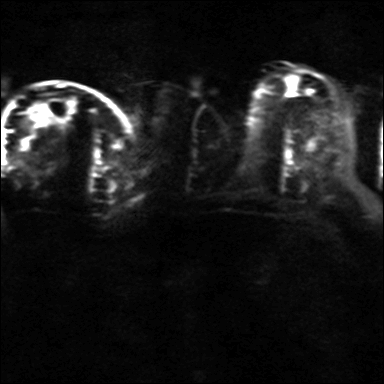
Breast MRI, one axial slice; slice 16 of 36 in the series (ordered by position); diffusion-weighted series; image 2 of 4 stored at this slice position (different b-values; order by instance number); 3 T; 4 mm slice thickness; 384 × 384 image matrix. Female patient.
Structures marked on this image (outlined manually by an expert reader):
- tumour on diffusion-weighted imaging: bounding box [x1, y1, x2, y2] px = [20, 139, 30, 147]